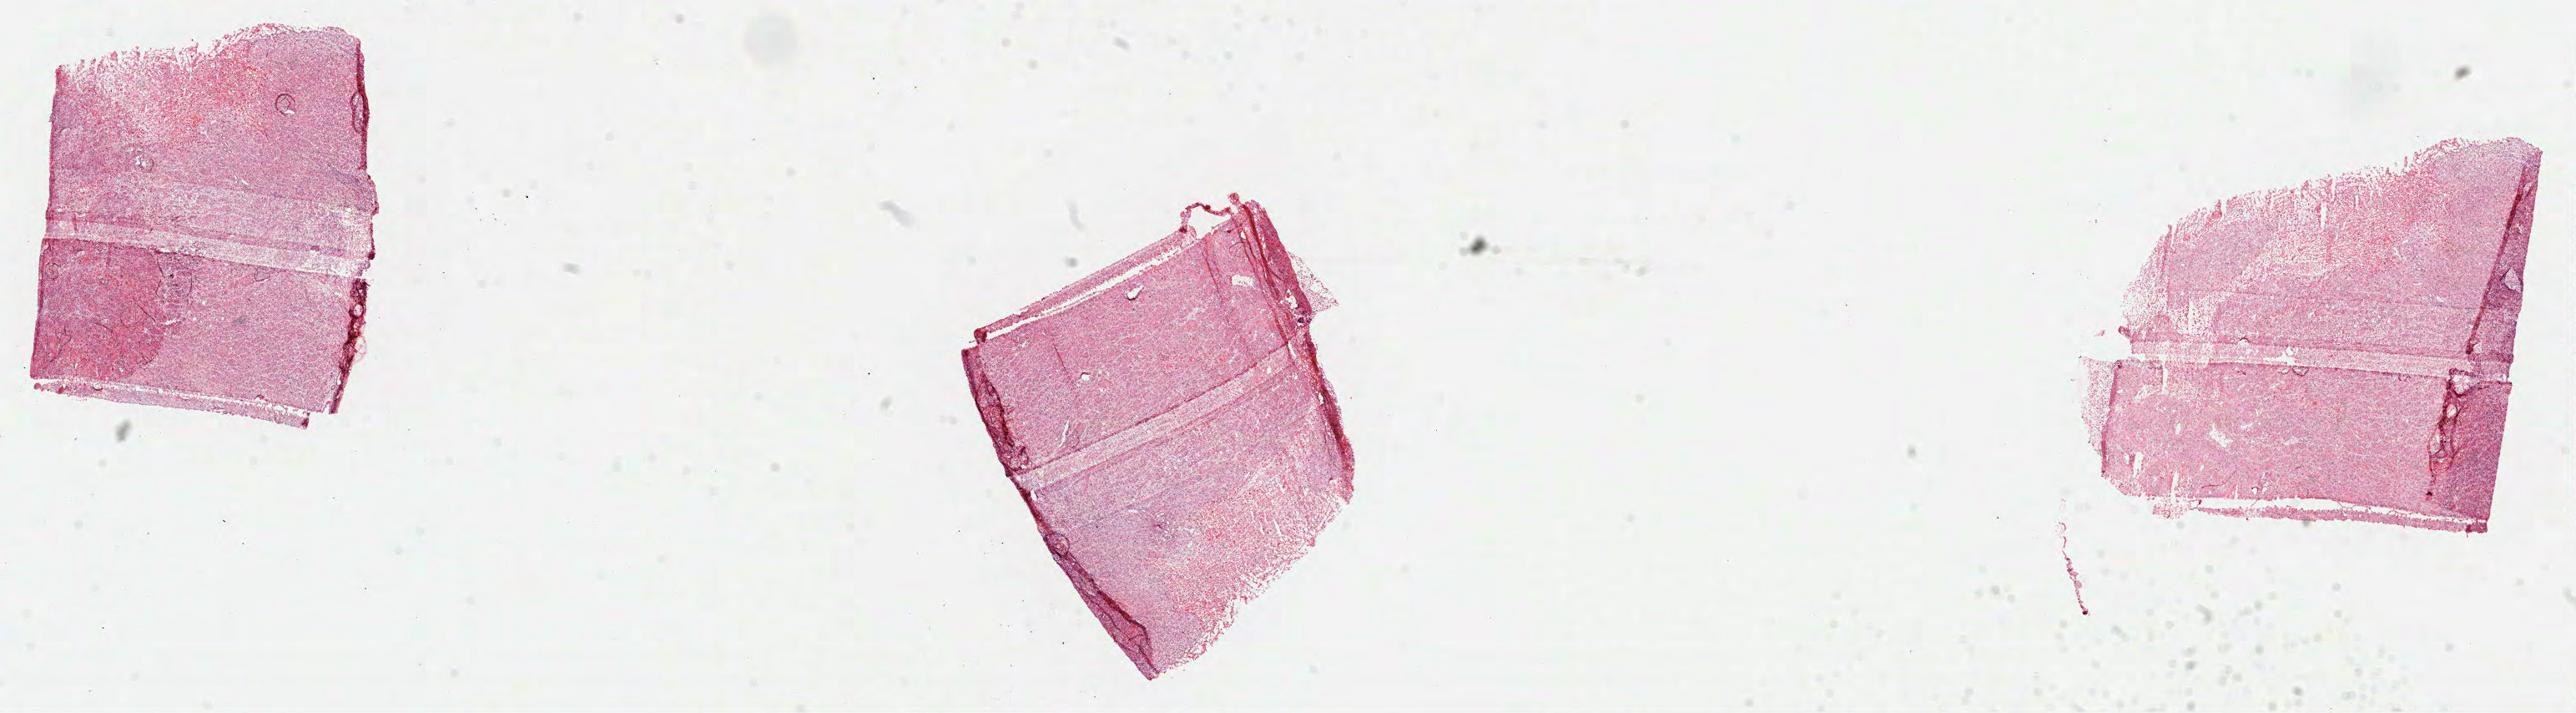
Whole-slide histology image, Hematoxylin and eosin (H&E) stained, shown as a low-resolution overview of the whole scanned area (about 24.9 x 6.9 mm, acquisition: 40x scan); formalin-fixed paraffin-embedded (FFPE) diagnostic section; sample: primary tumour, head and neck. Female patient; age at initial diagnosis 64 years.
Pathologic diagnosis: Squamous cell carcinoma, NOS (larynx, NOS).